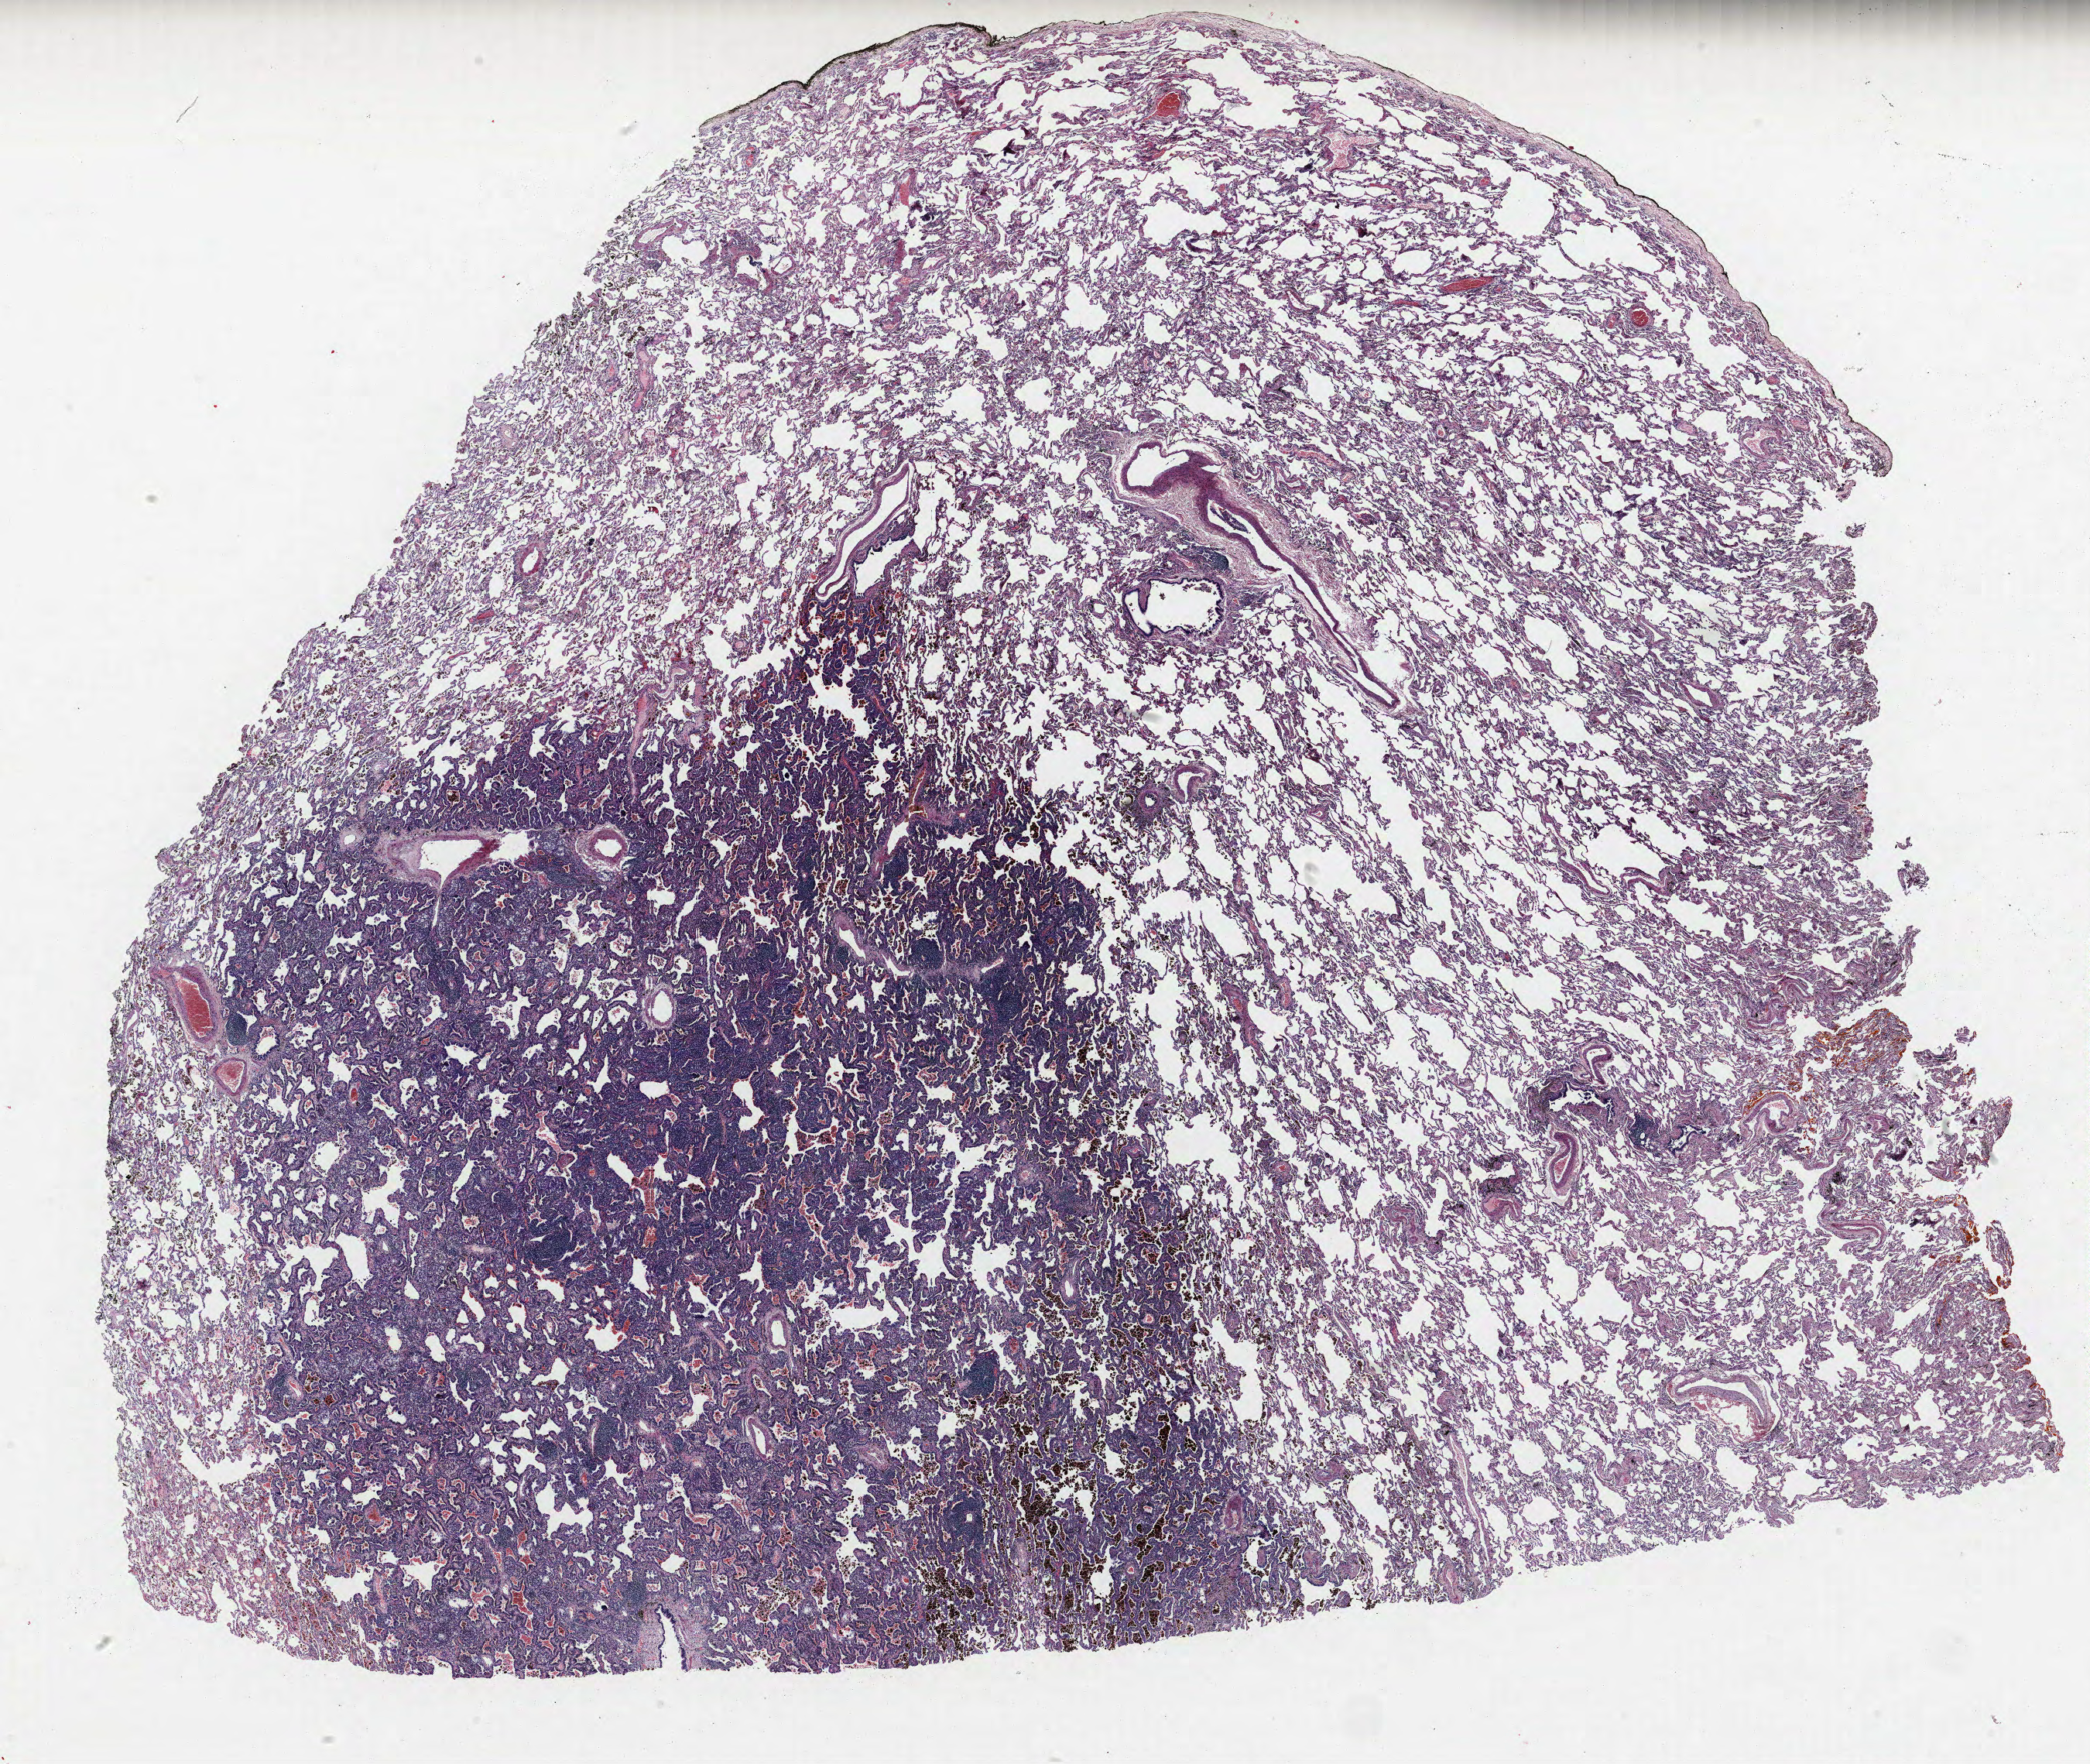
H&E-stained whole-slide image, a low-resolution overview of the entire scanned area, about 21.6 x 18.2 mm (from a 40x scan). FFPE section. Lung. Male patient, aged 60 at enrolment. Former smoker at enrolment. Grade: well differentiated (G1).
* ICD-O-3 topography: upper lobe of lung (C34.1)
* primary tumour location (clinical record): left upper lobe
* stage (AJCC 6th edition): IA
* tumour size (pathology): 16 mm
* participant's lung-cancer diagnosis: Bronchiolo-alveolar carcinoma, non-mucinous (ICD-O-3 8252/3)